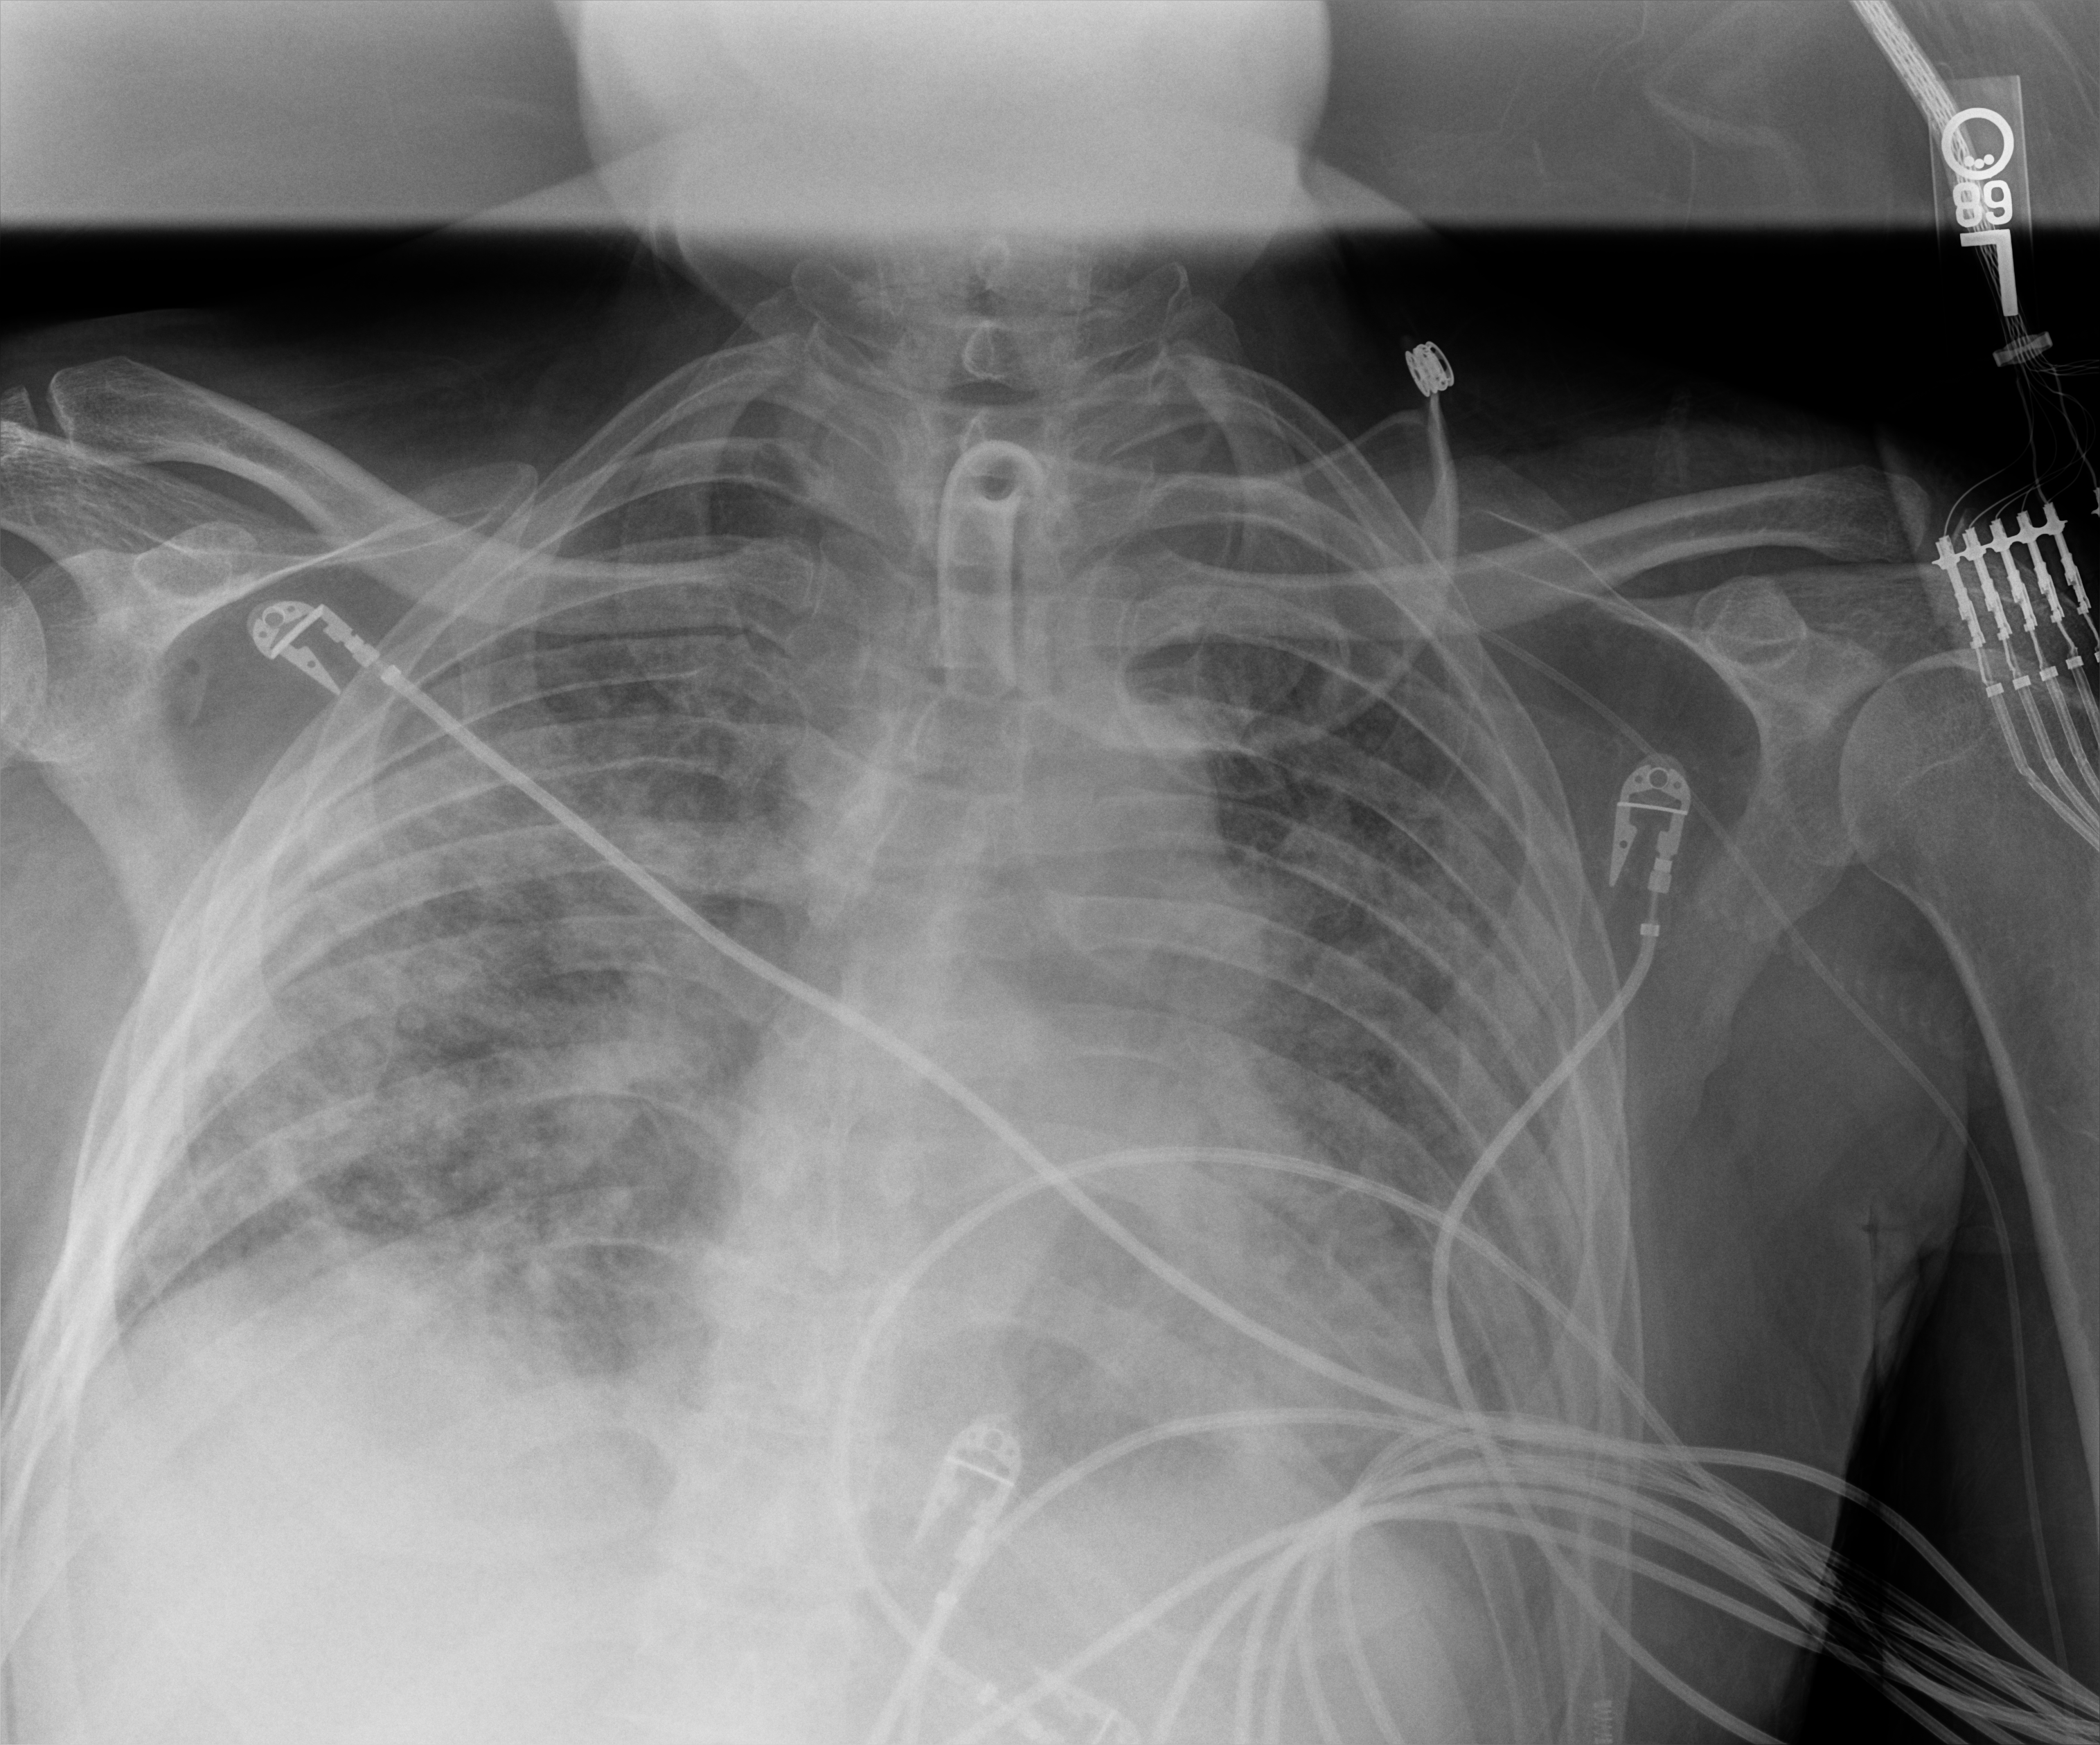
Portable chest radiograph, anteroposterior (AP) projection. Patient hospitalised with COVID-19; male, aged 18–59 years.
From the hospital-stay record, not from the radiograph (when in the stay this image was taken is not recorded):
- mechanically ventilated during this hospital stay: yes
- diabetes (admission record): no